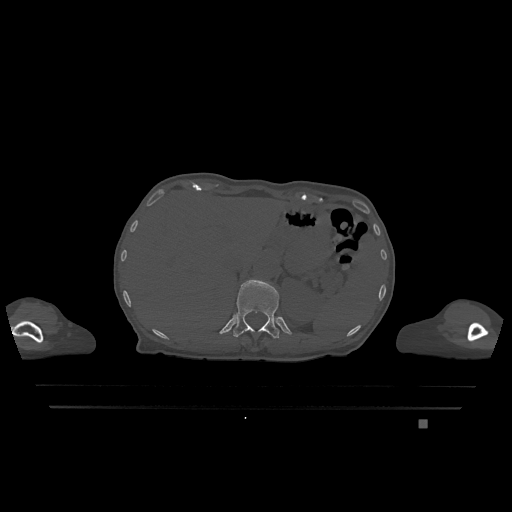
CT including the spine, one axial slice. Slice 536 of 1317 in the series (ordered by position). Bone window (W 1800 / L 400 HU). 0.5 mm slice thickness. 512 × 512 image matrix. Patient: female, 74 years. From the clinical record (not read from this slice): primary cancer: lung; vertebrae with lytic lesions (as recorded): T1, T4, T5, T6, L4, L5.
Outlined on this slice (semi-automatically segmented with operator editing):
- T12 vertebra: bounding box (x1, y1, x2, y2) in pixels: (233, 279, 279, 338)